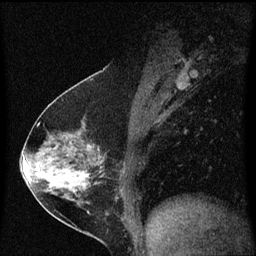
Breast MRI (dynamic contrast-enhanced), one sagittal slice. Position 31 of 60 along the scan axis. Dynamic contrast-enhanced series, image 2 of 3 at this slice position (ordered by acquisition). 1.5 T. TE 4.2 ms, TR 8.4 ms. 256 × 256 image matrix, field of view 200 × 200 mm. Female patient, age 54 years. Case-level facts recorded for this patient, not image findings: setting: breast cancer imaged before/during neoadjuvant chemotherapy; receptor status: HER2-positive.
Outlined on this slice (semi-automatically segmented with operator editing):
- analysis volume of interest (the breast-tissue region the enhancement analysis was run in; not a lesion): box from (x=32, y=122) to (x=121, y=213) px
- tumour enhancement mask (voxels above the 70 % enhancement threshold inside the analysis volume of interest): (x=68, y=172)–(x=89, y=179)